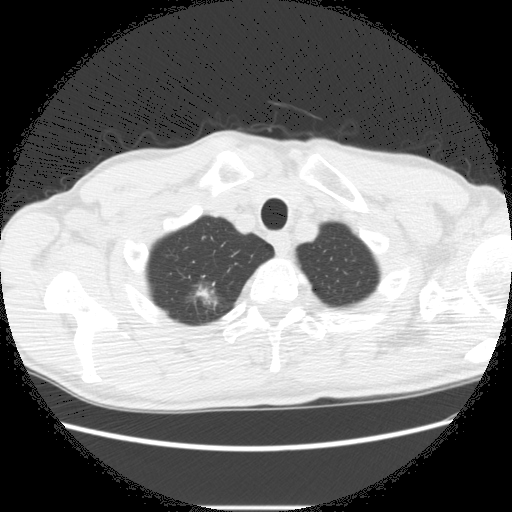
Low-dose screening chest CT, one axial slice; slice 259 of 282 in the series (ordered by position); reconstruction kernel STANDARD; 120 kVp; lung window (W 1500 / L -600 HU); 512 × 512 image matrix.
Structures marked on this image (expert manual segmentation):
- lesion 2 (nodule, upper lobe of right lung): bounding box [x1, y1, x2, y2] px = [194, 282, 219, 307]